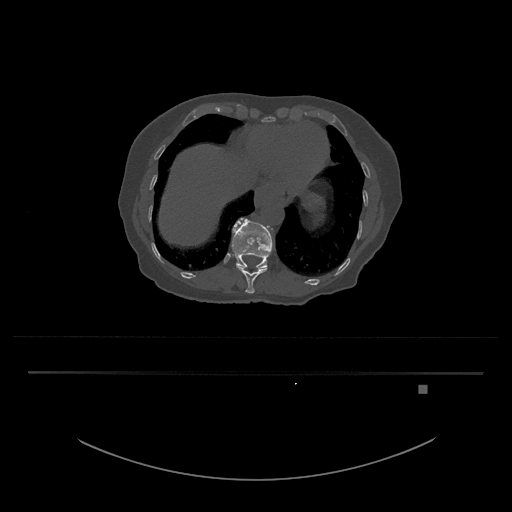
CT including the spine, one axial slice. Reconstruction kernel Br40s/3. 120 kVp. Bone window (W 1800 / L 400 HU). 0.5 mm slice thickness. 512 × 512 image matrix, field of view 500 × 500 mm. Female patient, age 57 years. Case-level facts recorded for this patient, not image findings: primary cancer: cervical.
Outlined on this slice (semi-automatically segmented with operator editing):
- T11 vertebra: box from (x=236, y=265) to (x=267, y=294) px
- T12 vertebra: (x=232, y=218)–(x=274, y=269)